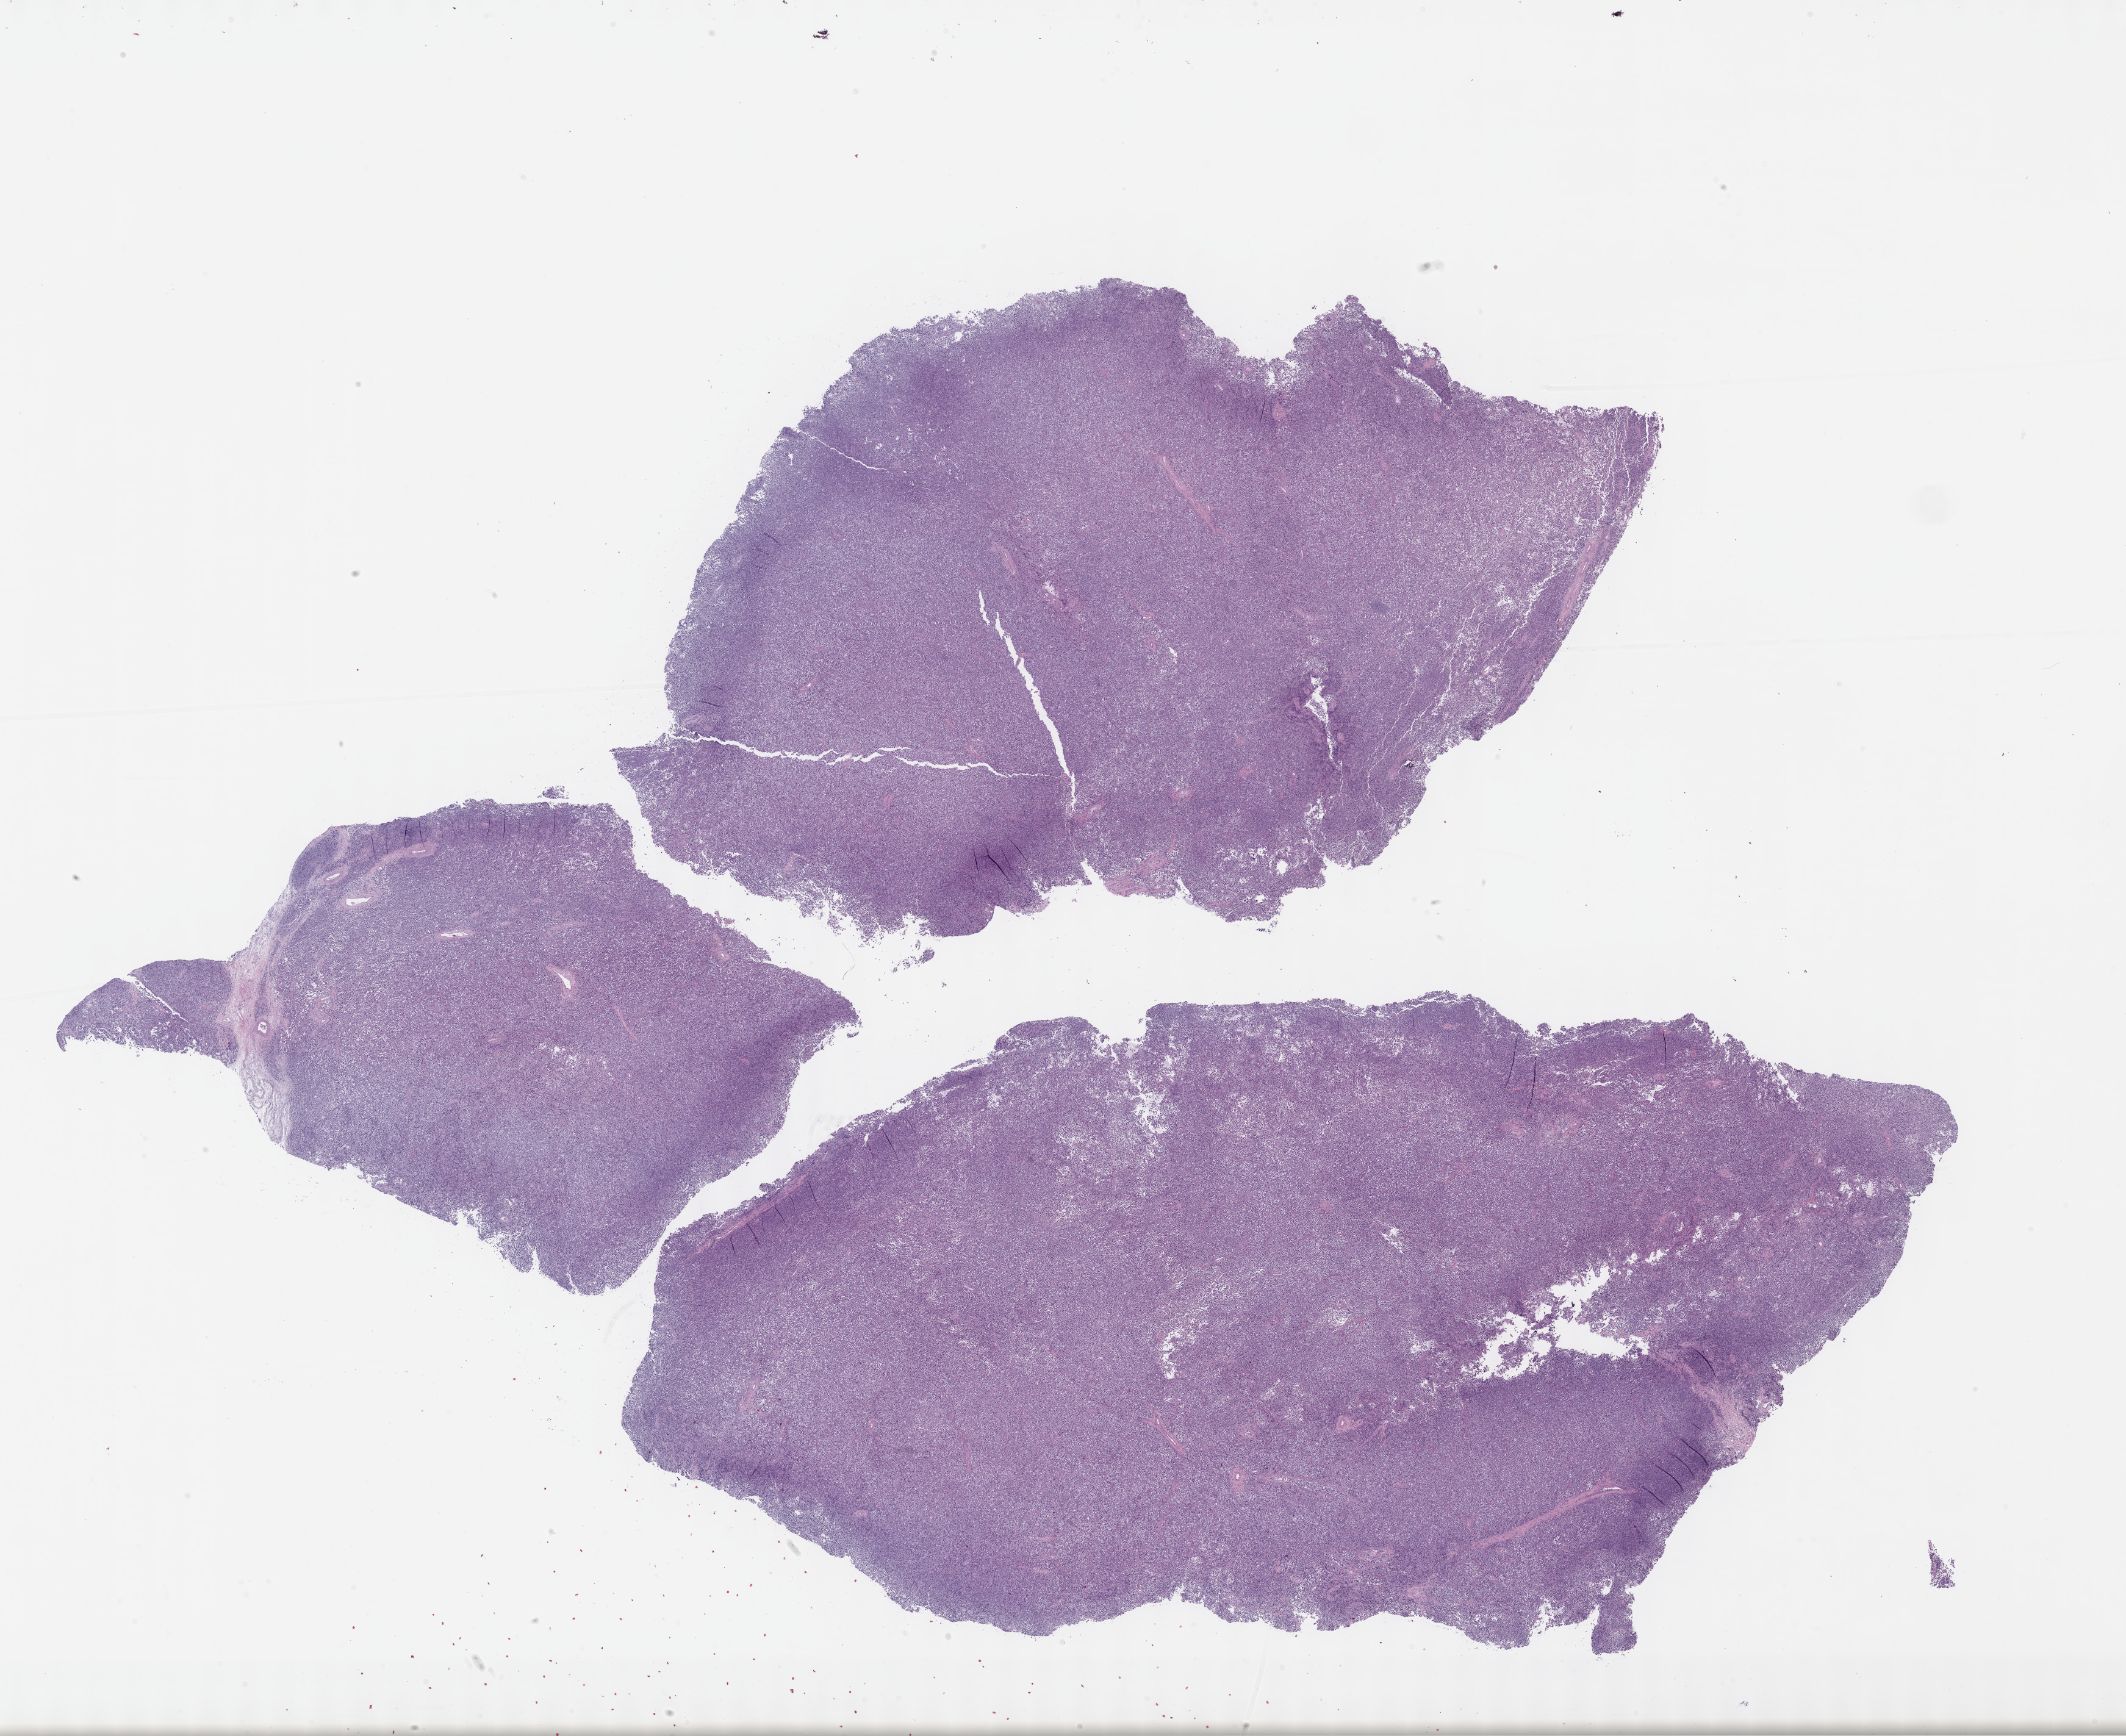
H&E-stained whole-slide image, low-resolution overview of the scanned area, about 28.2 x 23.0 mm (from a 40x scan). Formalin-fixed paraffin-embedded (FFPE) diagnostic section. Primary tumour sample from the testis. Male patient; age at initial diagnosis 22 years.
AJCC pathologic stage: IA. TNM: T1 NX M0. Laterality: right. Pathologic diagnosis: Seminoma, NOS.